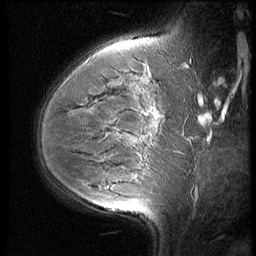
Breast MRI (dynamic contrast-enhanced), one sagittal slice; slice 42 of 60 in the series (ordered by position); 3 images stored at this slice position (order not interpretable as contrast timing); 1.5 T; TE 4.2 ms, TR 9 ms; 256 × 256 image matrix, field of view 180 × 180 mm. Female patient, age 35 years. From the clinical record (not read from this slice): setting: breast cancer imaged before/during neoadjuvant chemotherapy; receptor status: HR-positive, HER2-negative.
Outlined on this slice (semi-automatically segmented with operator editing):
- analysis volume of interest (the breast-tissue region the enhancement analysis was run in; not a lesion): bounding box <56,58,176,202> (left, top, right, bottom; pixels)
- tumour enhancement mask (voxels above the 140 % enhancement threshold inside the analysis volume of interest): <146,114,158,119>